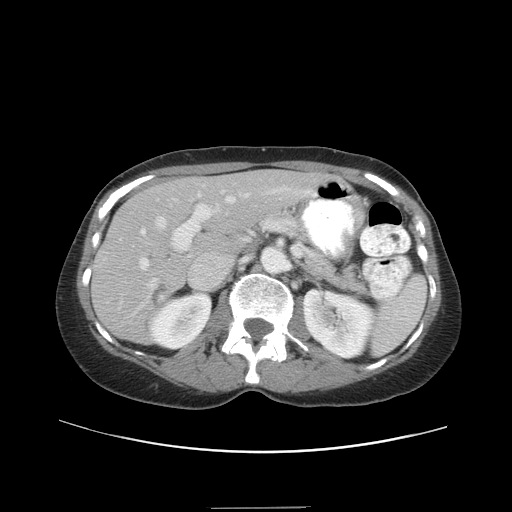
Contrast-enhanced abdominal CT, one axial slice; position 22 of 38 along the scan axis; reconstruction kernel STANDARD; 120 kVp; intravenous contrast given; soft-tissue window (W 400 / L 40 HU); 5 mm slice thickness; 512 × 512 image matrix, field of view 388 × 388 mm. Female patient, age 64 years. Case-level facts recorded for this patient, not image findings: diagnosis: colorectal cancer liver metastases, imaged before liver resection; multiple liver metastases: no; largest metastasis: 3.8 cm; disease in both lobes: yes.
Outlined on this slice (manually delineated by an expert):
- hepatic veins: box from (x=129, y=193) to (x=249, y=317) px
- liver: (x=93, y=170)–(x=320, y=343)
- planned liver remnant (the part of the liver to remain after resection): (x=136, y=170)–(x=320, y=249)
- portal vein (with intrahepatic branches): (x=140, y=190)–(x=228, y=270)